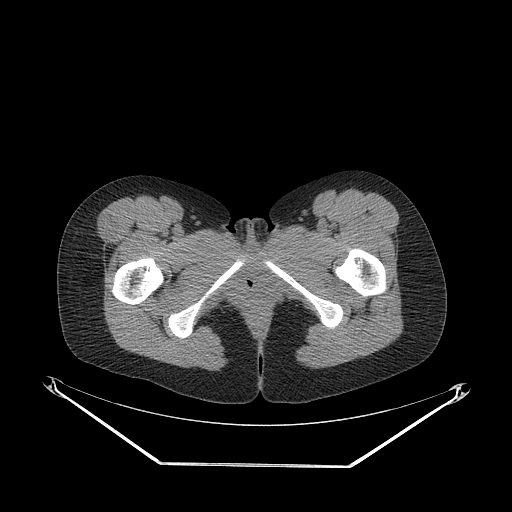
CT of an extremity soft-tissue mass (from a PET/CT study), one axial slice. Position 52 of 267 along the scan axis. Reconstruction kernel STANDARD. 140 kVp. Soft-tissue window (W 400 / L 40 HU). 3.75 mm slice thickness. 512 × 512 image matrix, field of view 500 × 500 mm. Female patient. Case-level facts recorded for this patient, not image findings: histological type: synovial sarcoma; grade: intermediate; site of the primary tumour: right thigh.
Annotated regions visible in this slice (expert contour drawn on MRI and transferred to this co-registered scan by the dataset authors):
- gross tumour volume including surrounding oedema: box from (x=94, y=217) to (x=115, y=243) px
- gross tumour volume (mass): (x=94, y=217)–(x=115, y=243)